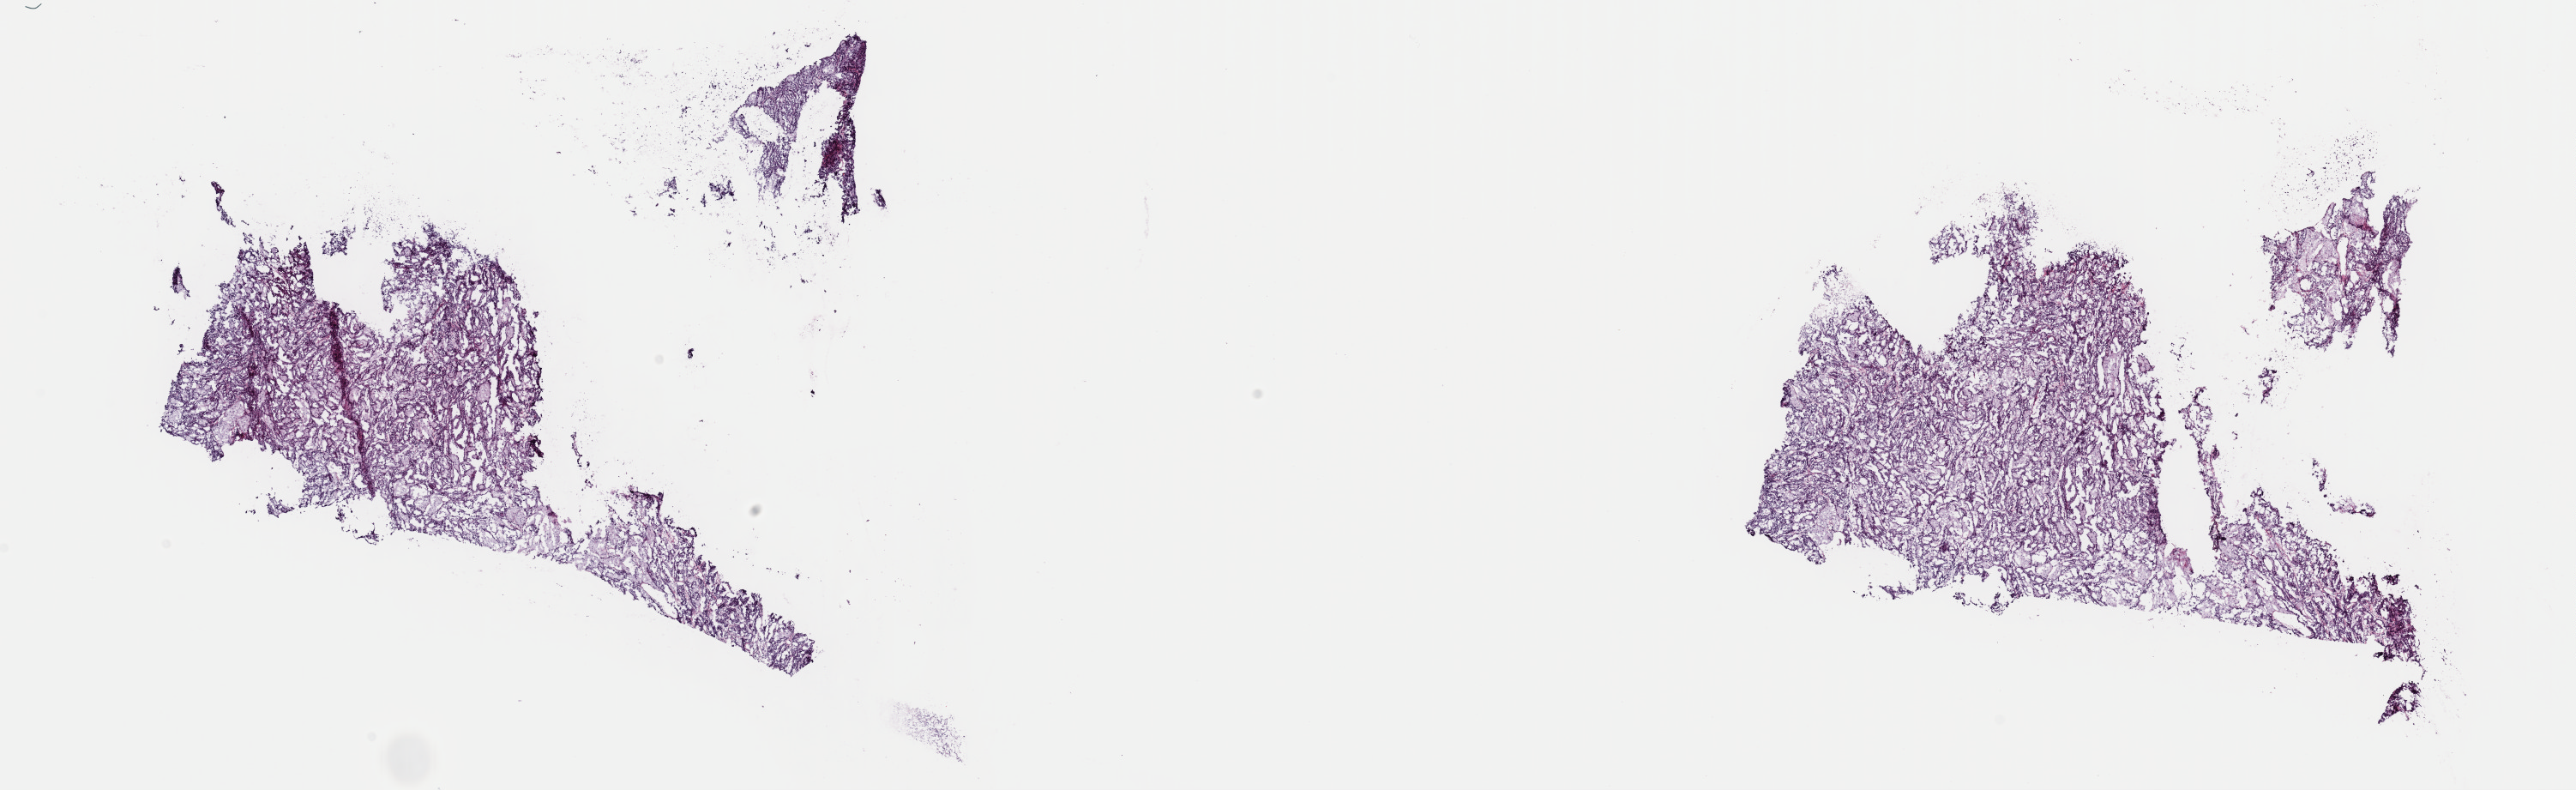
Digitized H&E-stained tissue section (whole slide) — shown as a low-resolution overview of the whole scanned area (about 23.7 x 7.3 mm, from a 40x scan), frozen section, sample: primary tumour, kidney. Patient: male, age at initial diagnosis 54 years. Pathologist review of this section (percent, as recorded): tumour cells 80%, tumour nuclei 80%, normal cells 0%, stromal cells 20%, necrosis 0%. Inflammatory infiltration, as recorded: lymphocyte infiltration 3%, monocyte infiltration 5%, neutrophil infiltration 0%.
AJCC pathologic stage: I (7th edition). Diagnosis: Papillary adenocarcinoma, NOS.